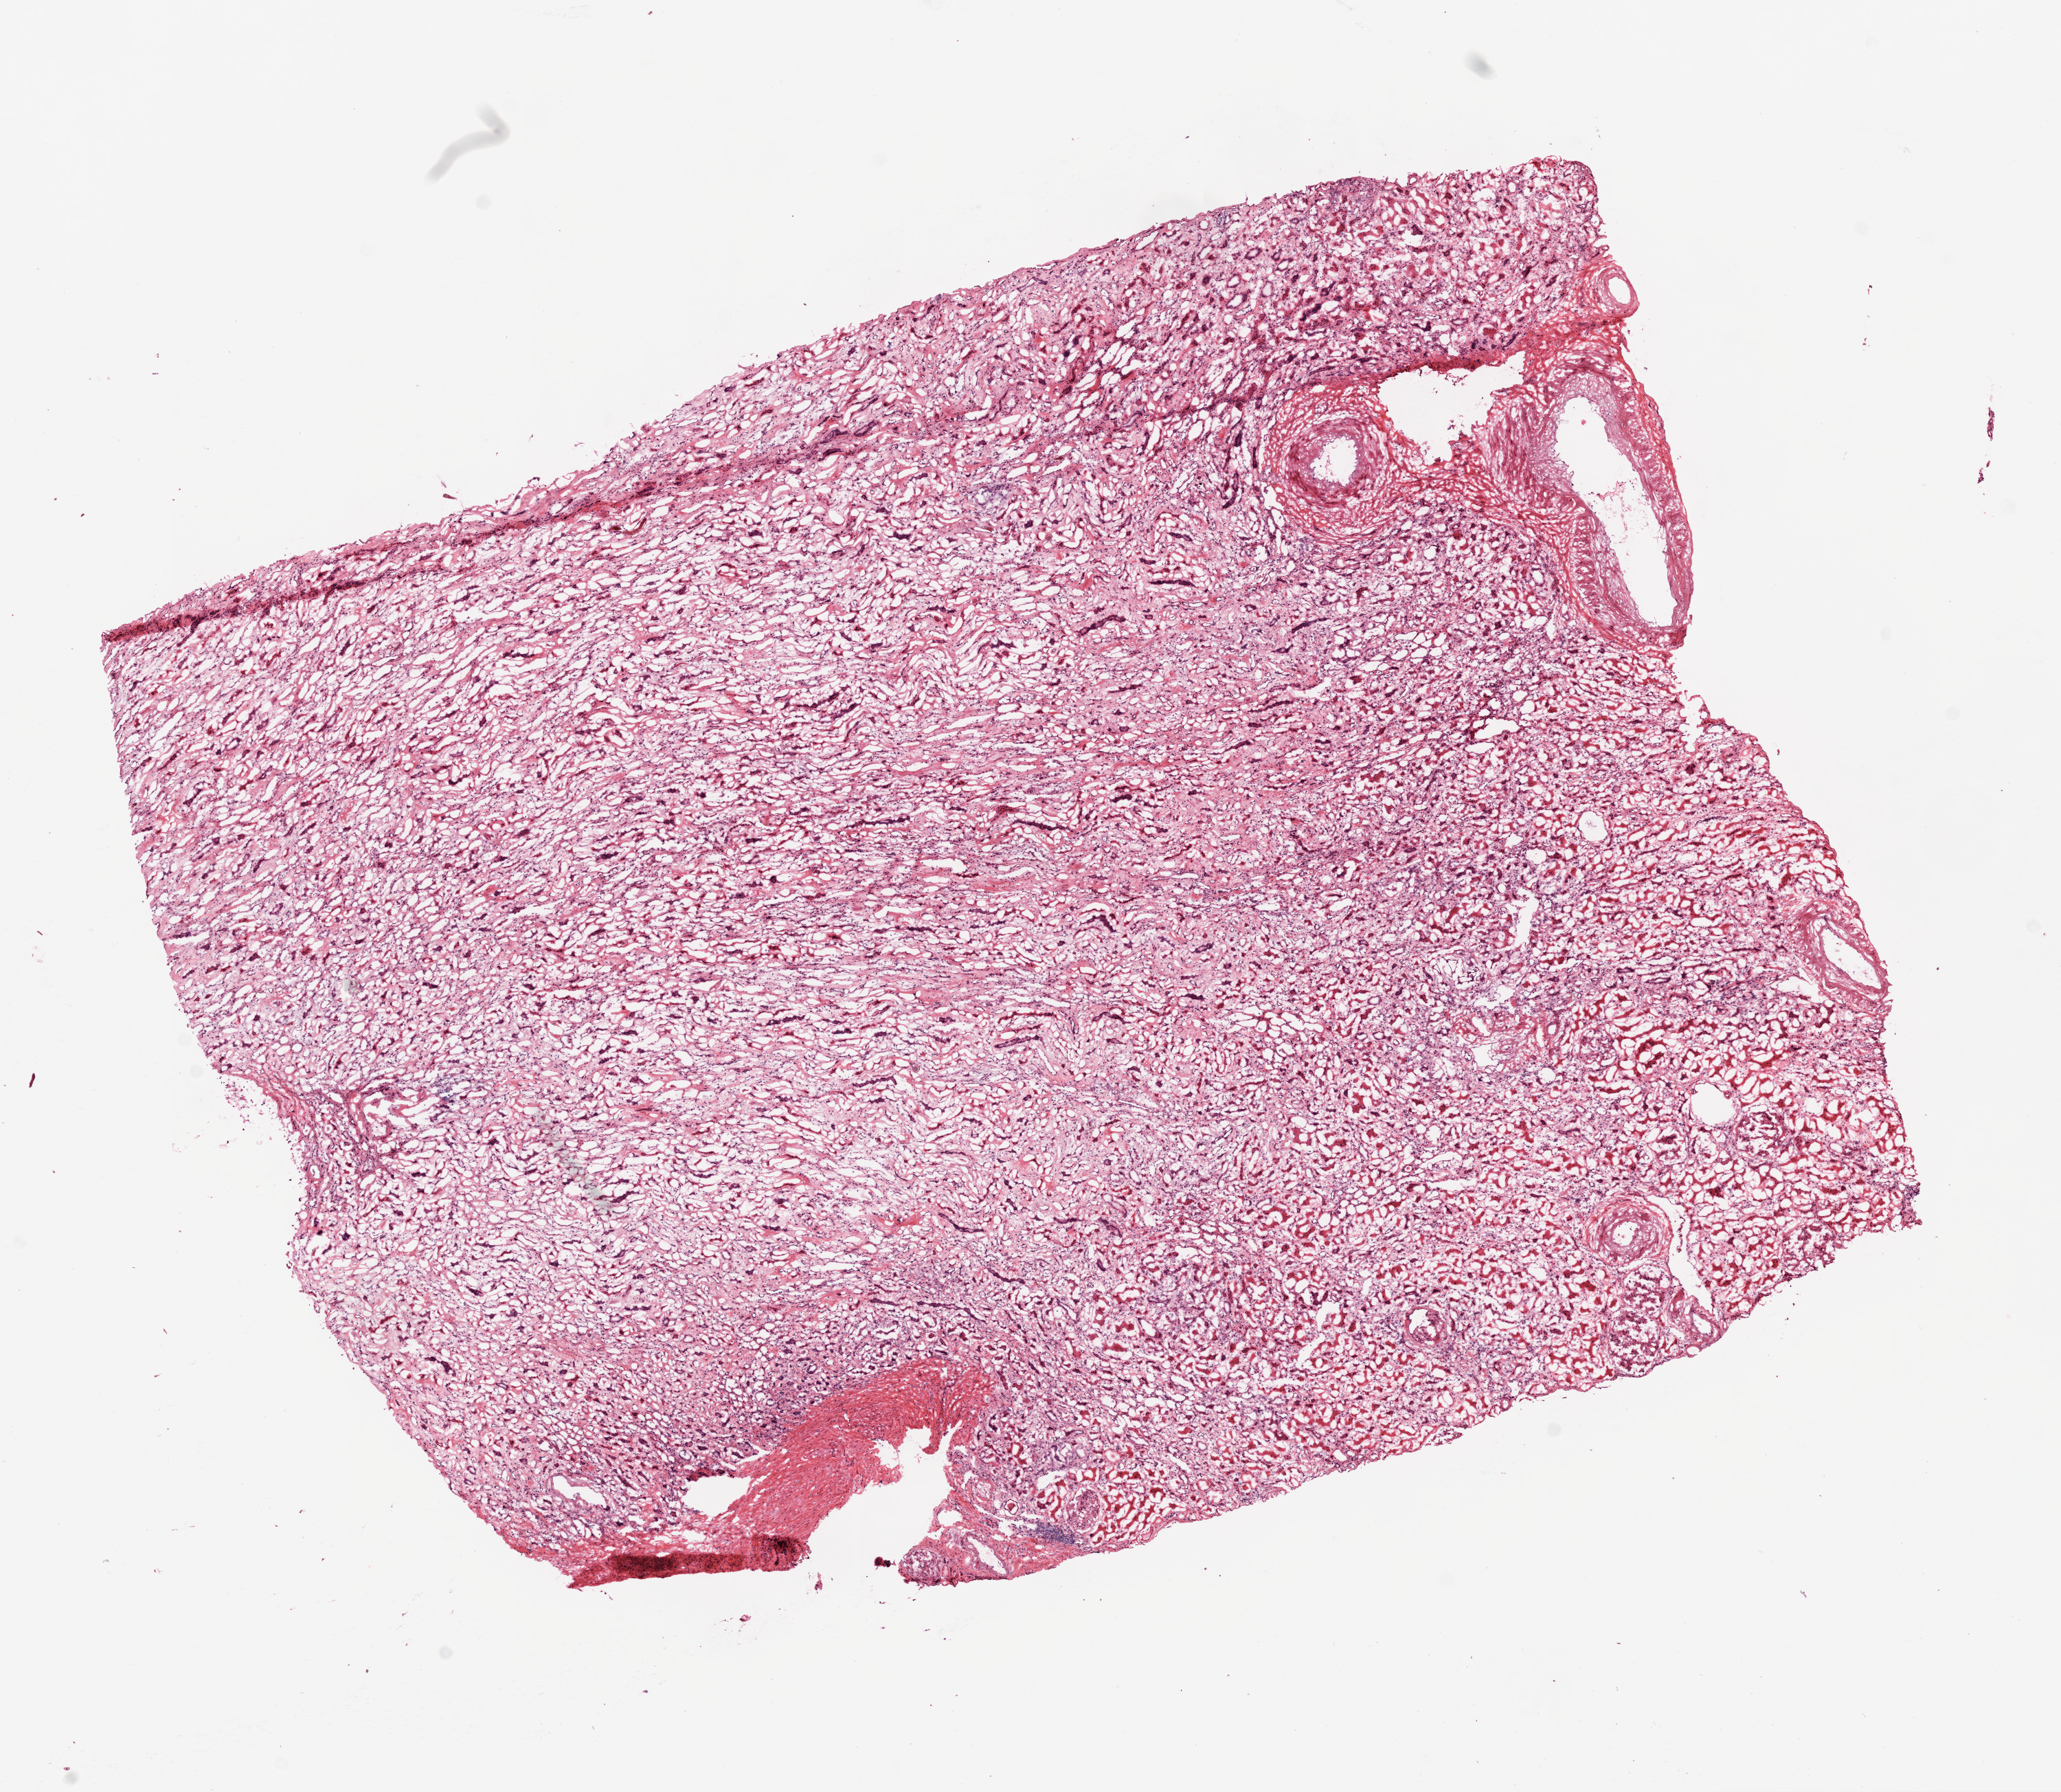
Whole-slide histology image, H&E-stained, shown as a low-resolution overview of the whole scanned area (about 12.0 x 10.5 mm, from a 20x scan), frozen section from the top of the tissue portion, kidney, solid tissue normal (non-tumour tissue) sample. Male, age 63 years at initial diagnosis.
This section: solid tissue normal sample (biorepository sample class). Patient diagnosis: Clear cell adenocarcinoma, NOS.